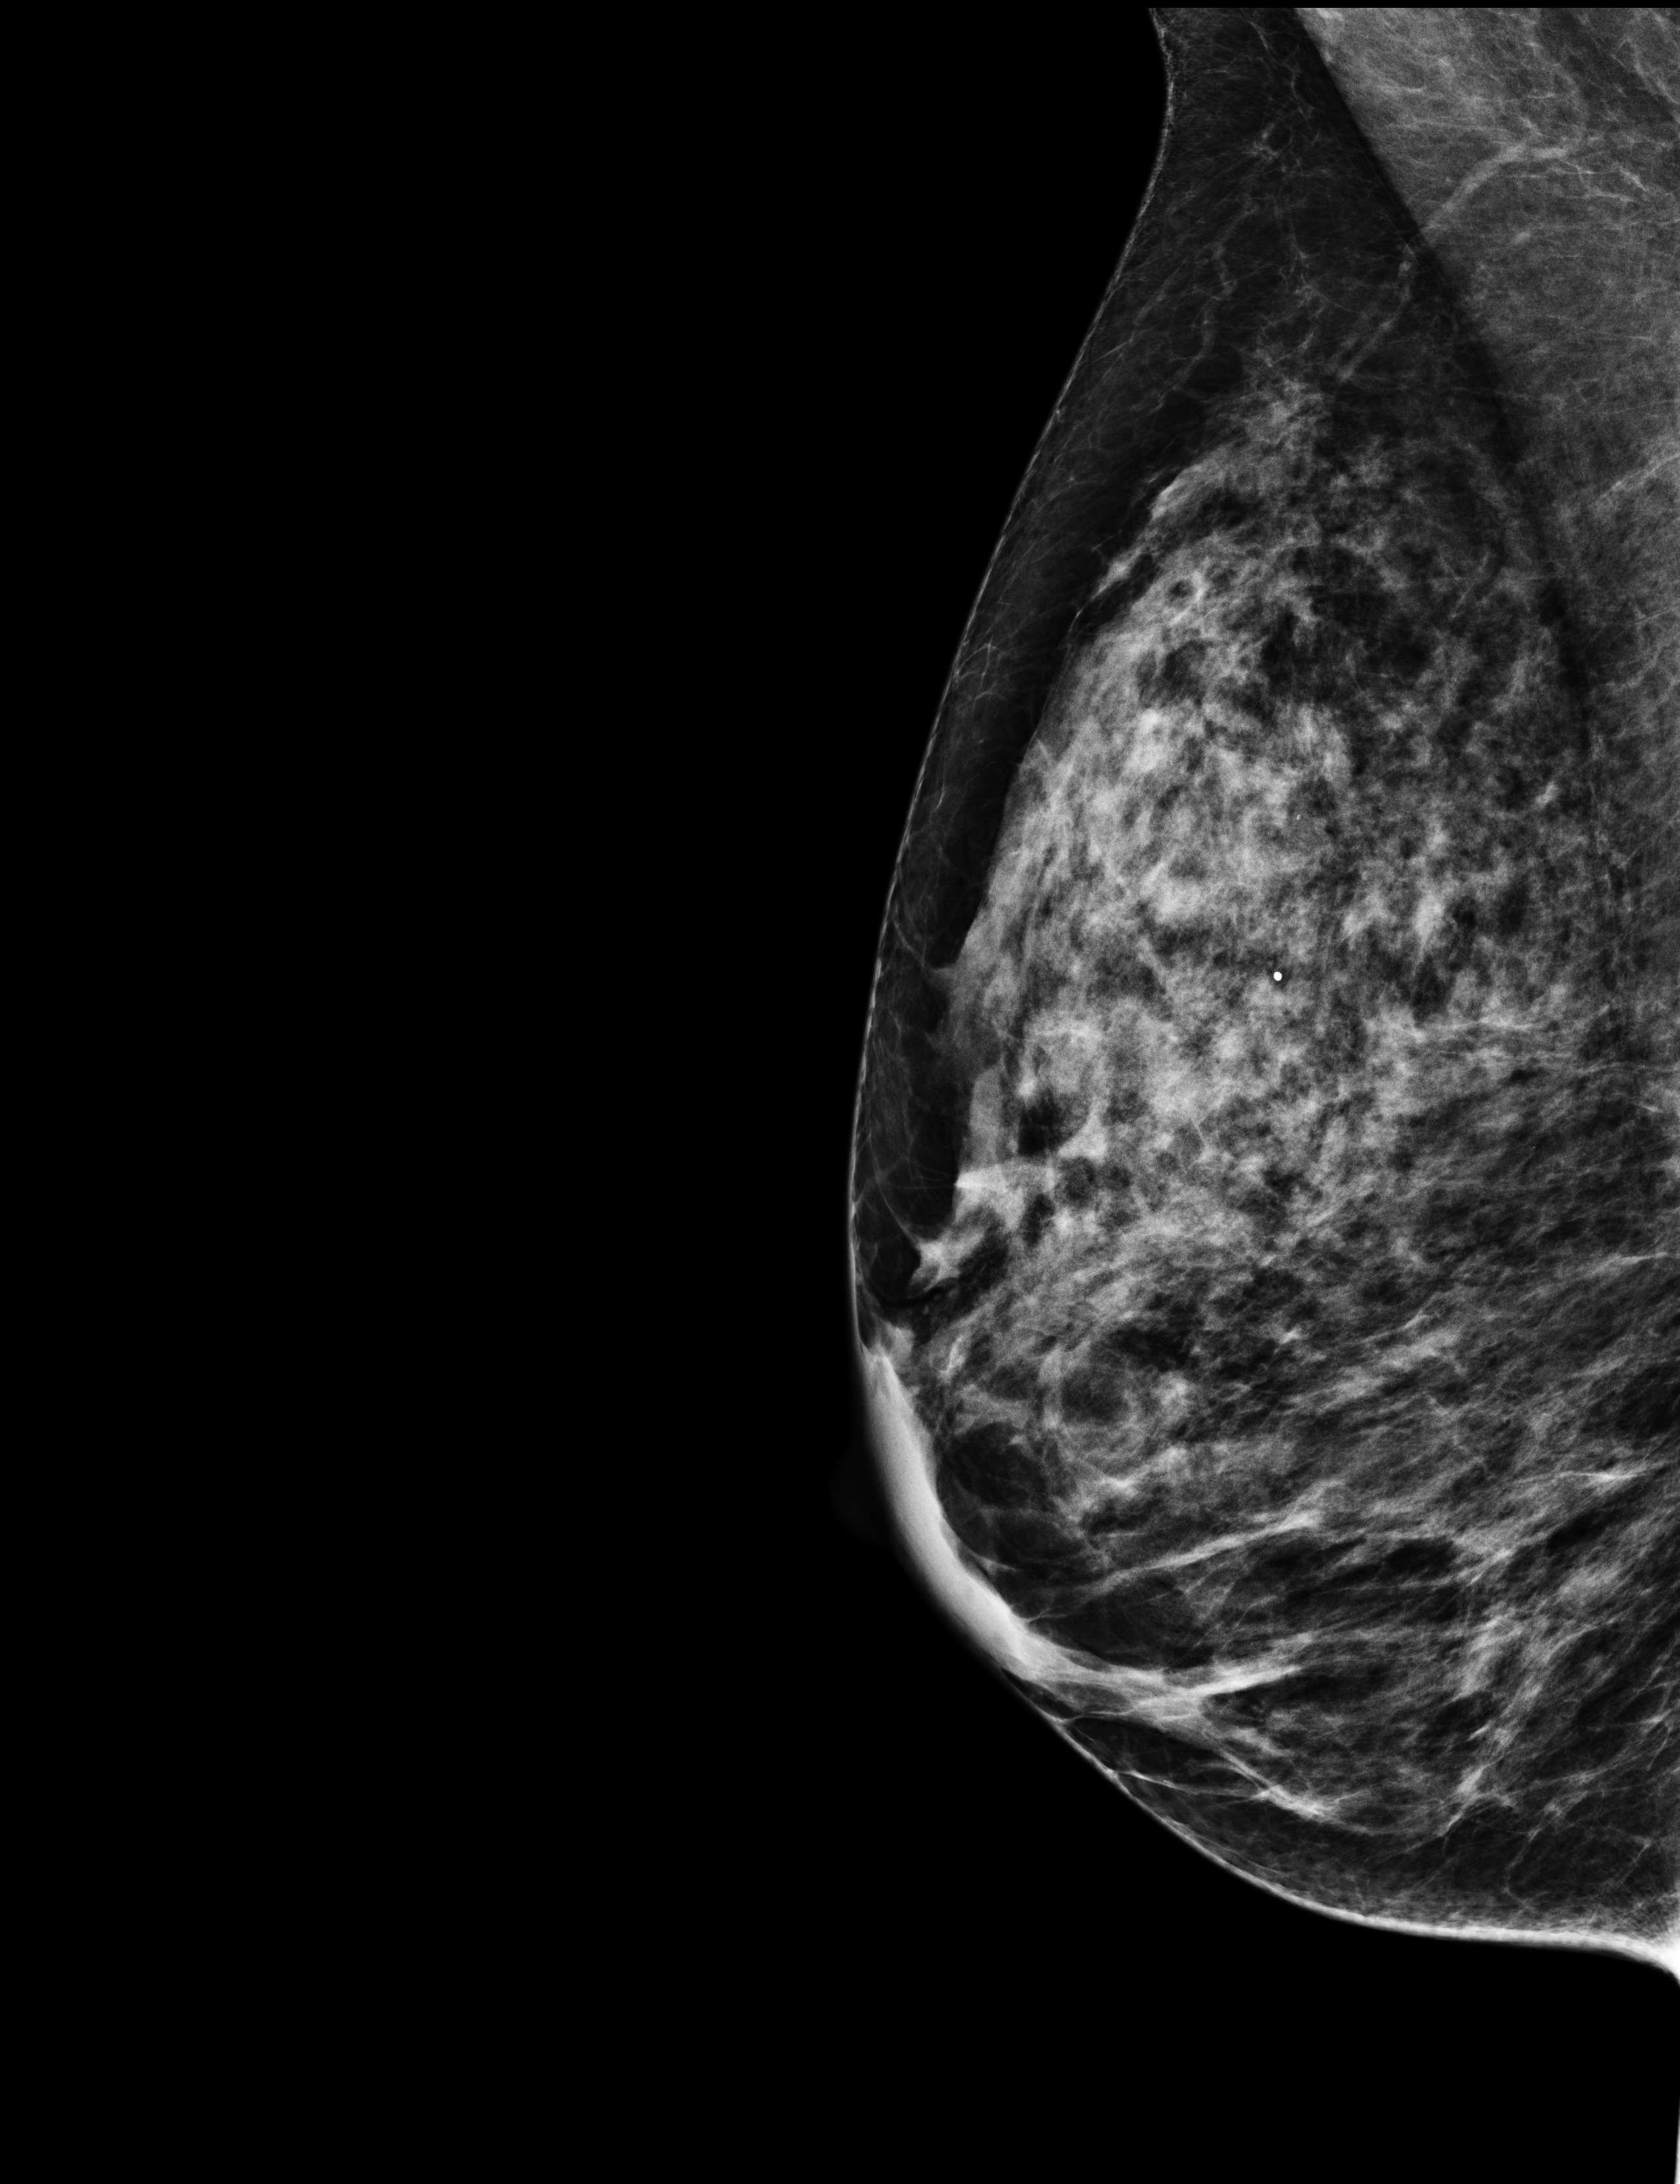
Screening examination, compressed breast thickness 52 mm.
Image type: full-field digital mammogram. Breast: right. Projection: medio-lateral oblique projection.